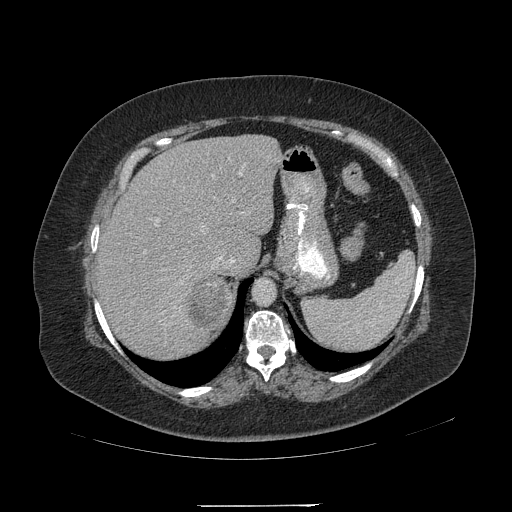
Contrast-enhanced abdominal CT, one axial slice. Position 163 of 217 along the scan axis. Soft-tissue window (W 400 / L 40 HU). 1.25 mm slice thickness. 512 × 512 image matrix, field of view 453 × 453 mm. Female patient, age 55 years. From the clinical record (not read from this slice): diagnosis: adrenocortical carcinoma; tumour side: right adrenal; tumour size at pathology: 11 cm; Ki-67 index: 20 %; stage (as recorded): 2.
Outlined on this slice (semi-automatic segmentation, software-assisted and operator-edited):
- mass: bounding box <188,278,227,328> (left, top, right, bottom; pixels)